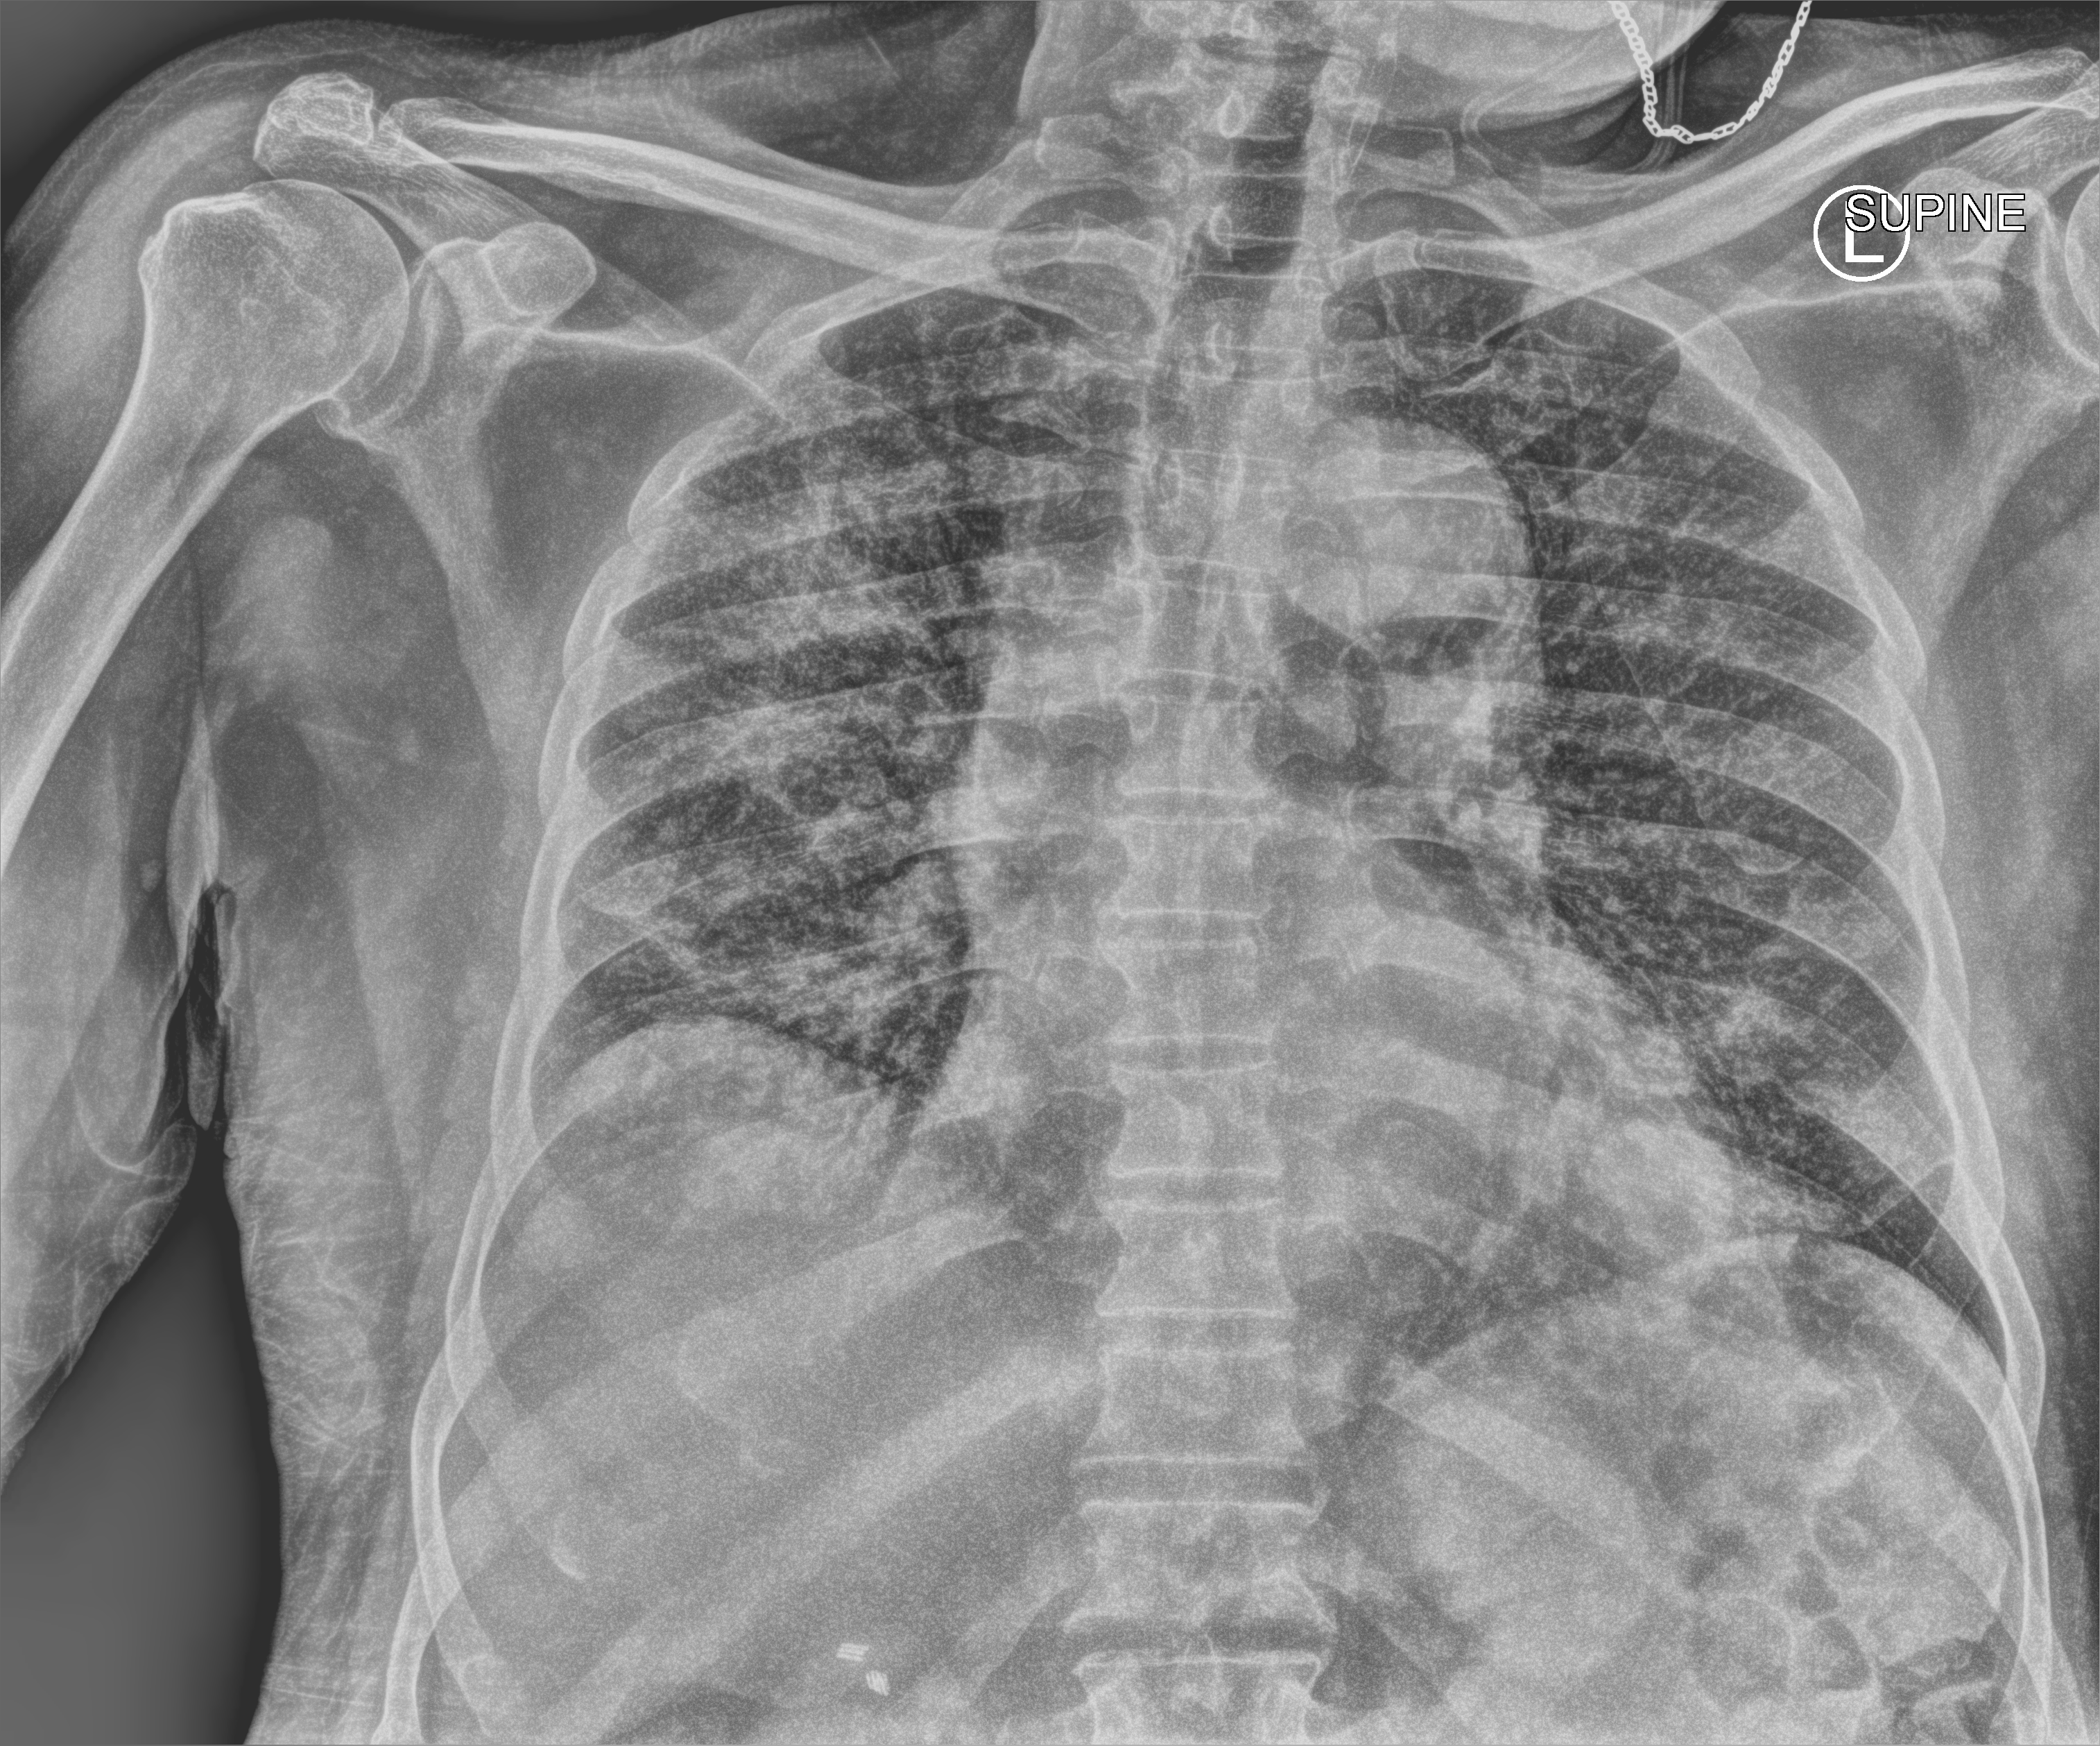
Portable chest radiograph. Patient hospitalised with COVID-19; male, aged 60–74 years.
Admission-level facts for this patient (not findings on this image; timing relative to this image not recorded): hypertension (admission record): yes.